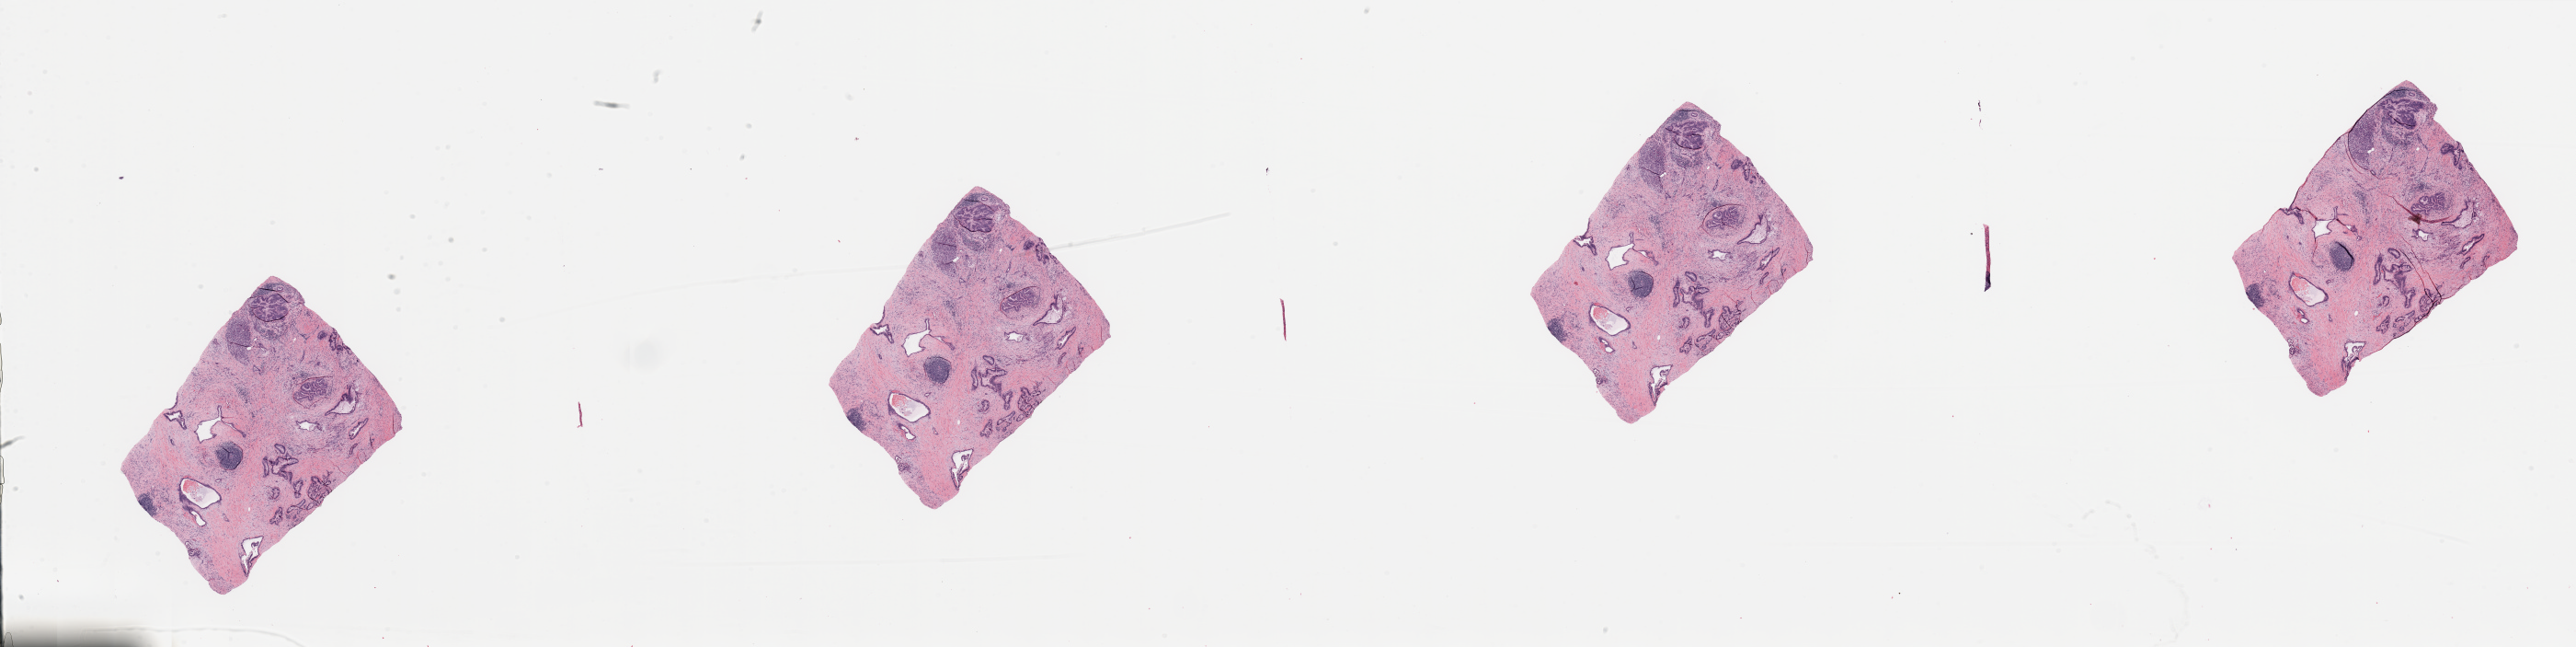
Whole-slide histology image, H&E, whole scanned area (about 44.3 x 11.1 mm, acquisition: 20x scan) shown as a low-resolution overview. Tumour tissue sample, sampled site: pancreas. Female, 78 y/o. Histologic grade: G2 (moderately differentiated). Composition of this section per pathologist review: tumour nuclei 20%, necrosis 0%.
Primary tumour site (as recorded): head. AJCC pathologic stage: IIB. Diagnosis: Infiltrating duct carcinoma, NOS.